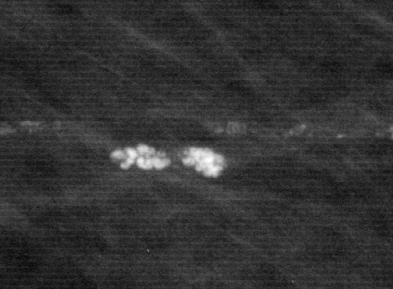
Cropped region of a digitized screen-film mammogram centred on a radiologist-marked abnormality, left breast, CC view.
Calcifications, morphology pleomorphic, distribution clustered; BI-RADS assessment category 4; pathology (as recorded): benign.